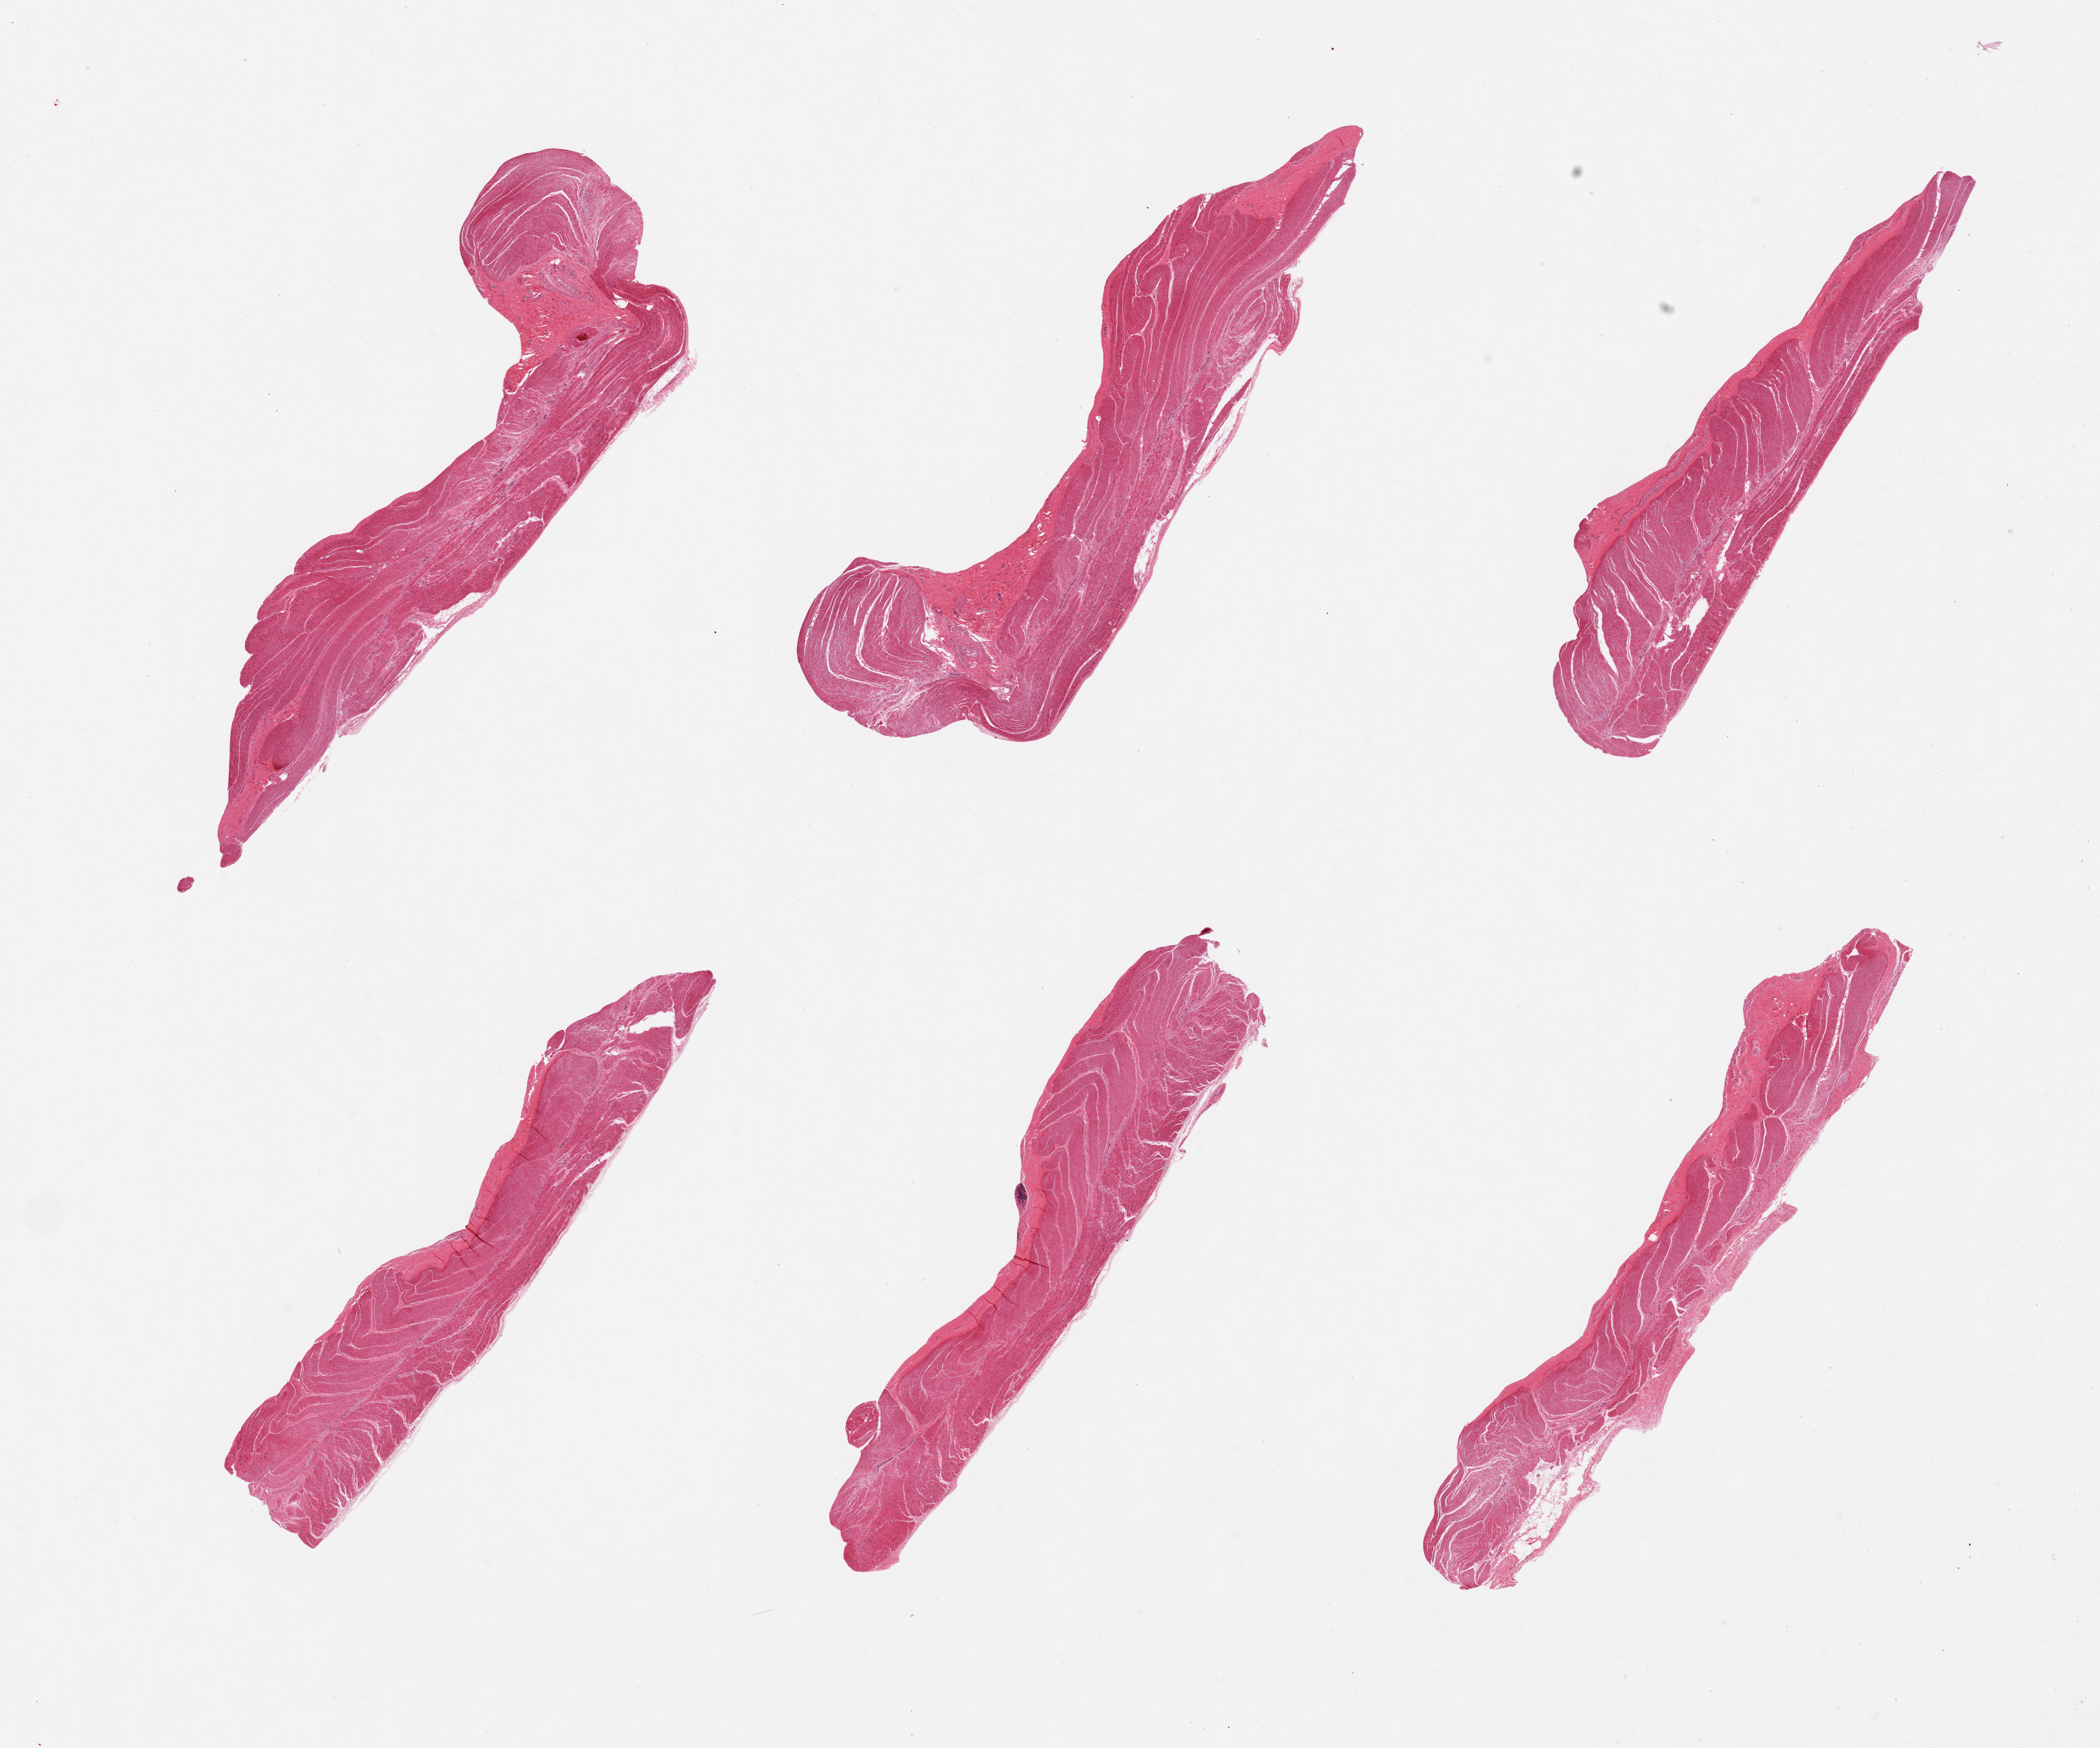
Digitized H&E-stained section, whole scanned area (about 24.6 x 20.5 mm) shown as a low-resolution overview, PAXgene-fixed, paraffin-embedded tissue, section of sigmoid colon (target tissue), tissue donor sample. Female donor.
- review note (as recorded): 6 pieces, all muscularis, good specimens